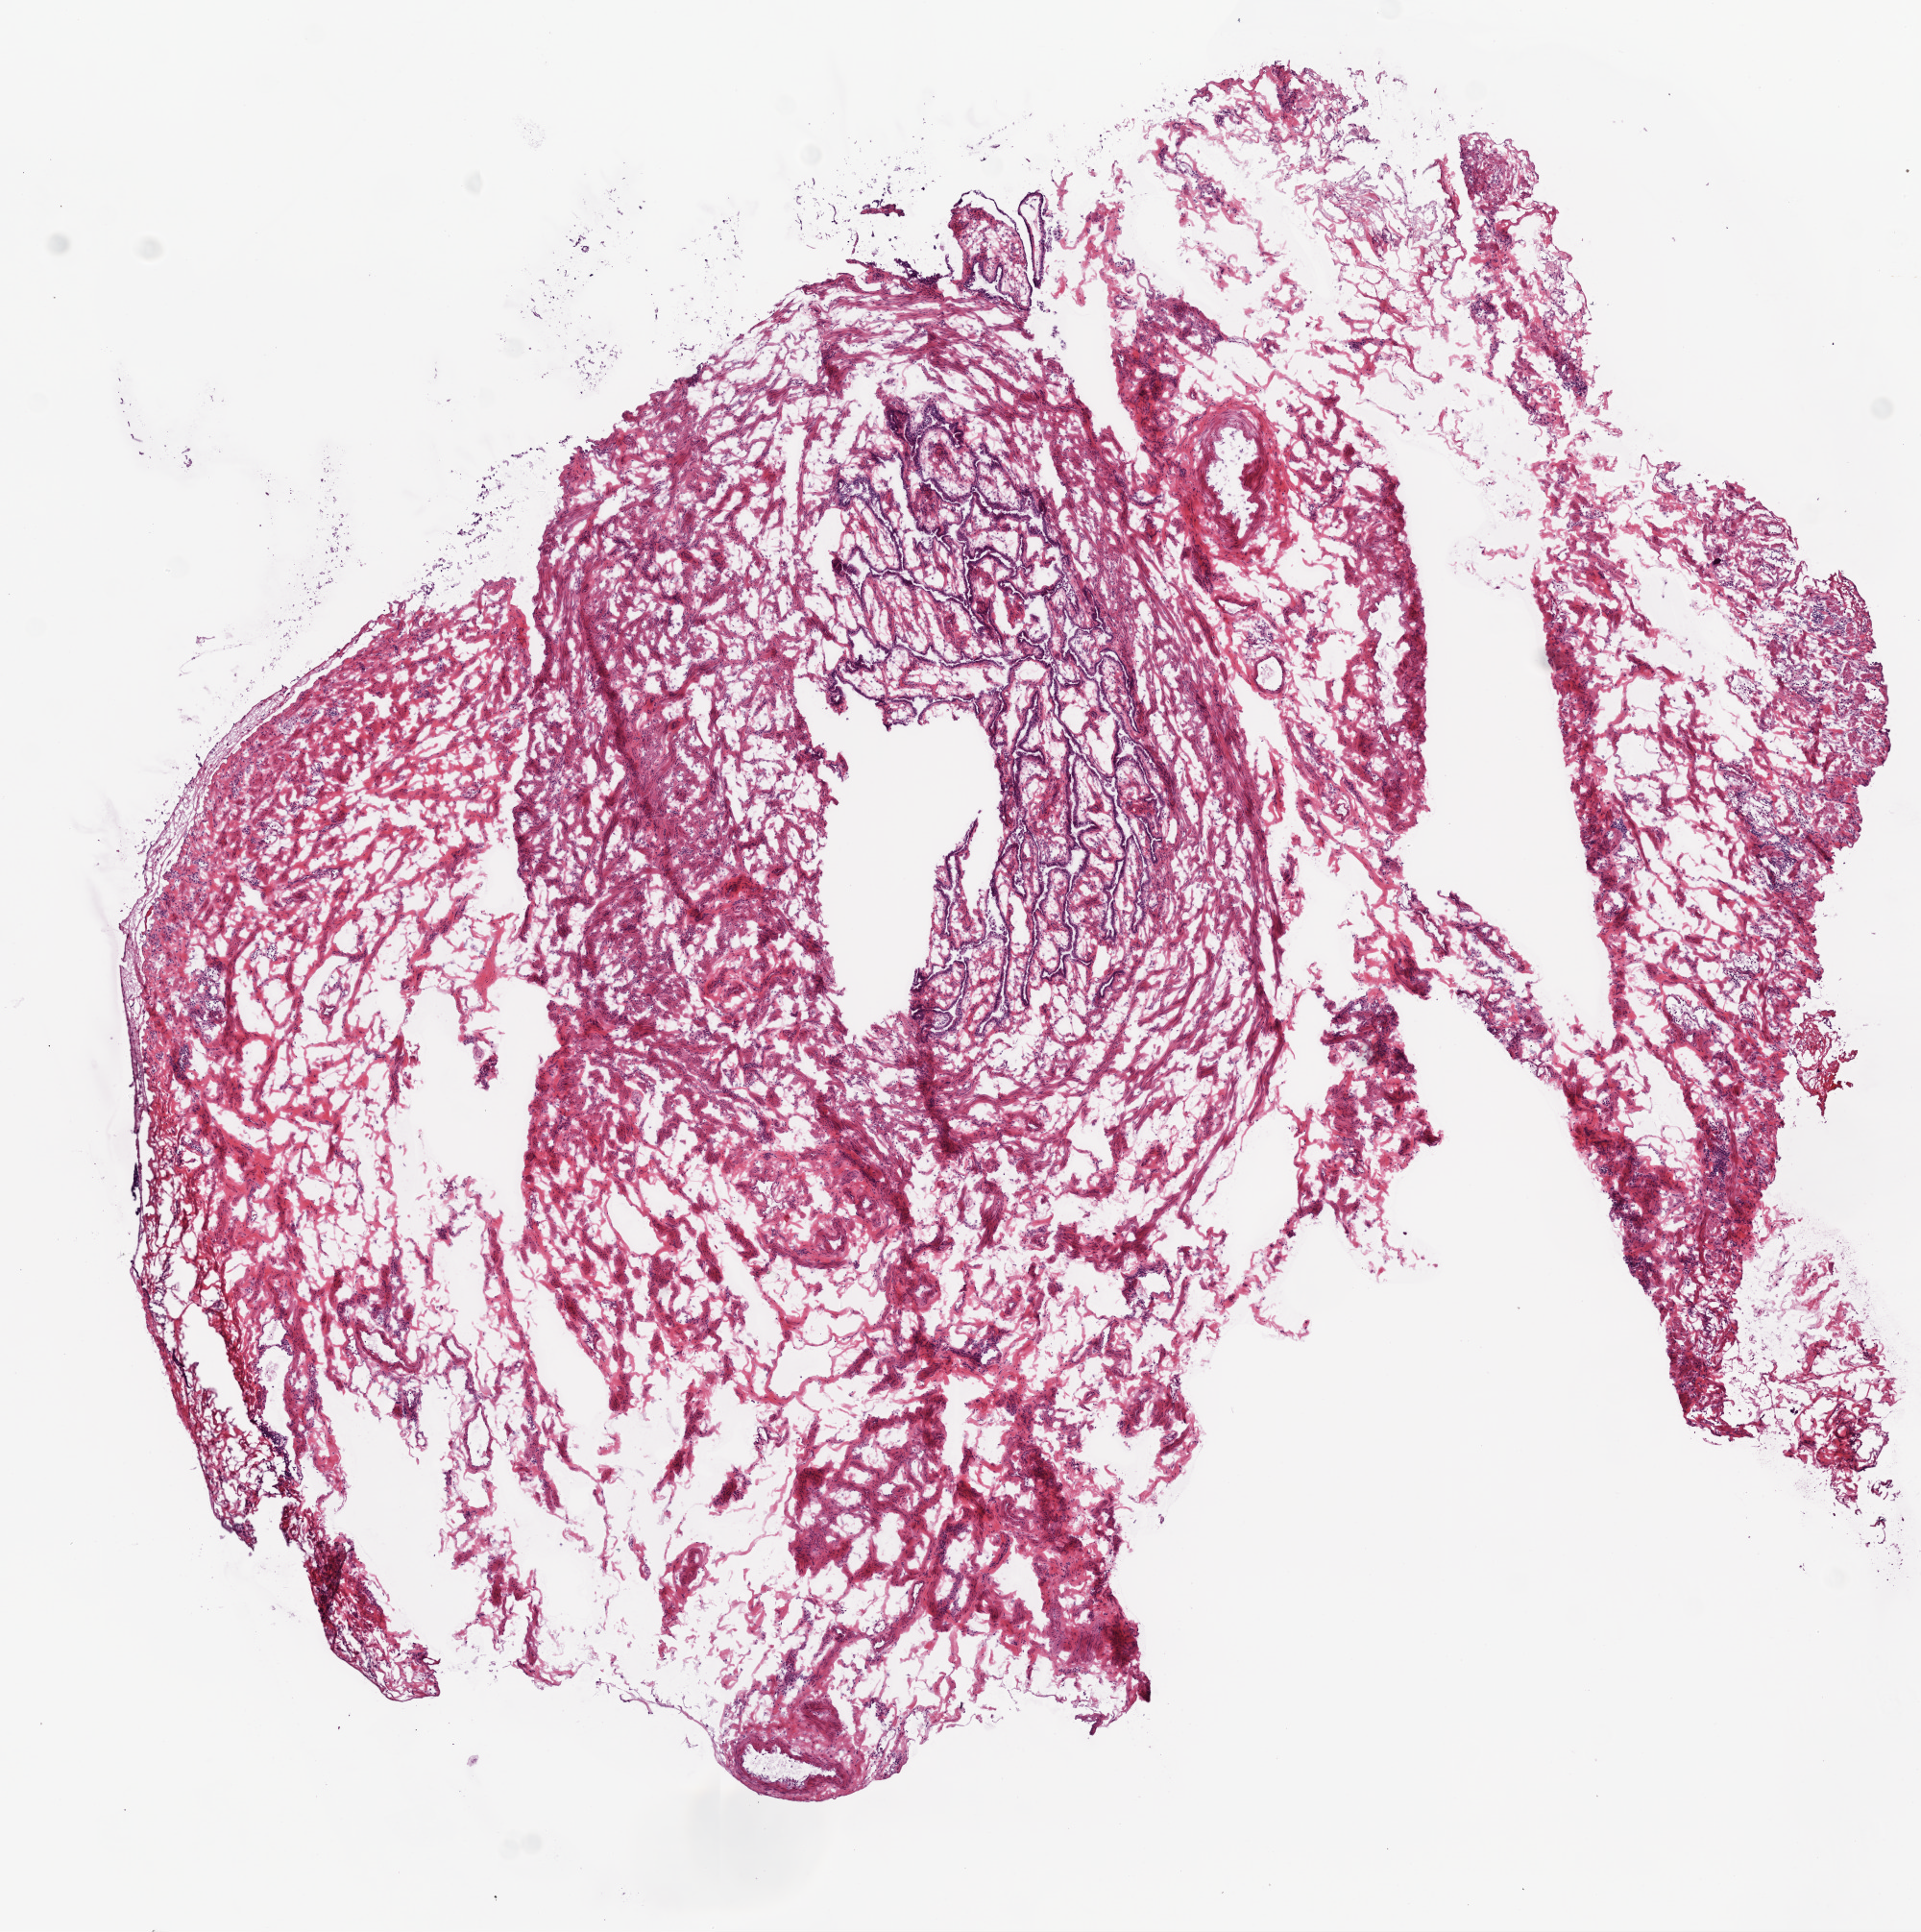
H&E-stained whole-slide image — low-resolution overview of the scanned area, about 8.0 x 8.1 mm (slide scanned at 20x); frozen section from the bottom of the tissue portion; ovary, solid tissue normal (non-tumour tissue) sample. Female, age 45 years at initial diagnosis.
This section: solid tissue normal (non-tumour) sample from the same patient. Patient diagnosis: Serous cystadenocarcinoma, NOS.